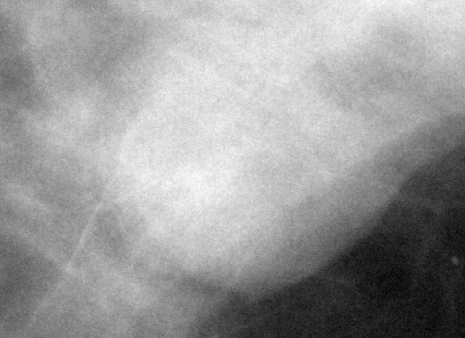
Crop from a digitized film mammogram around one marked abnormality; right breast; CC view.
Finding: mass, shape oval, margins circumscribed; BI-RADS assessment category 4; subtlety rating 5 on a 1 (subtle) to 5 (obvious) scale; pathology result (as recorded, not read from the image): benign.